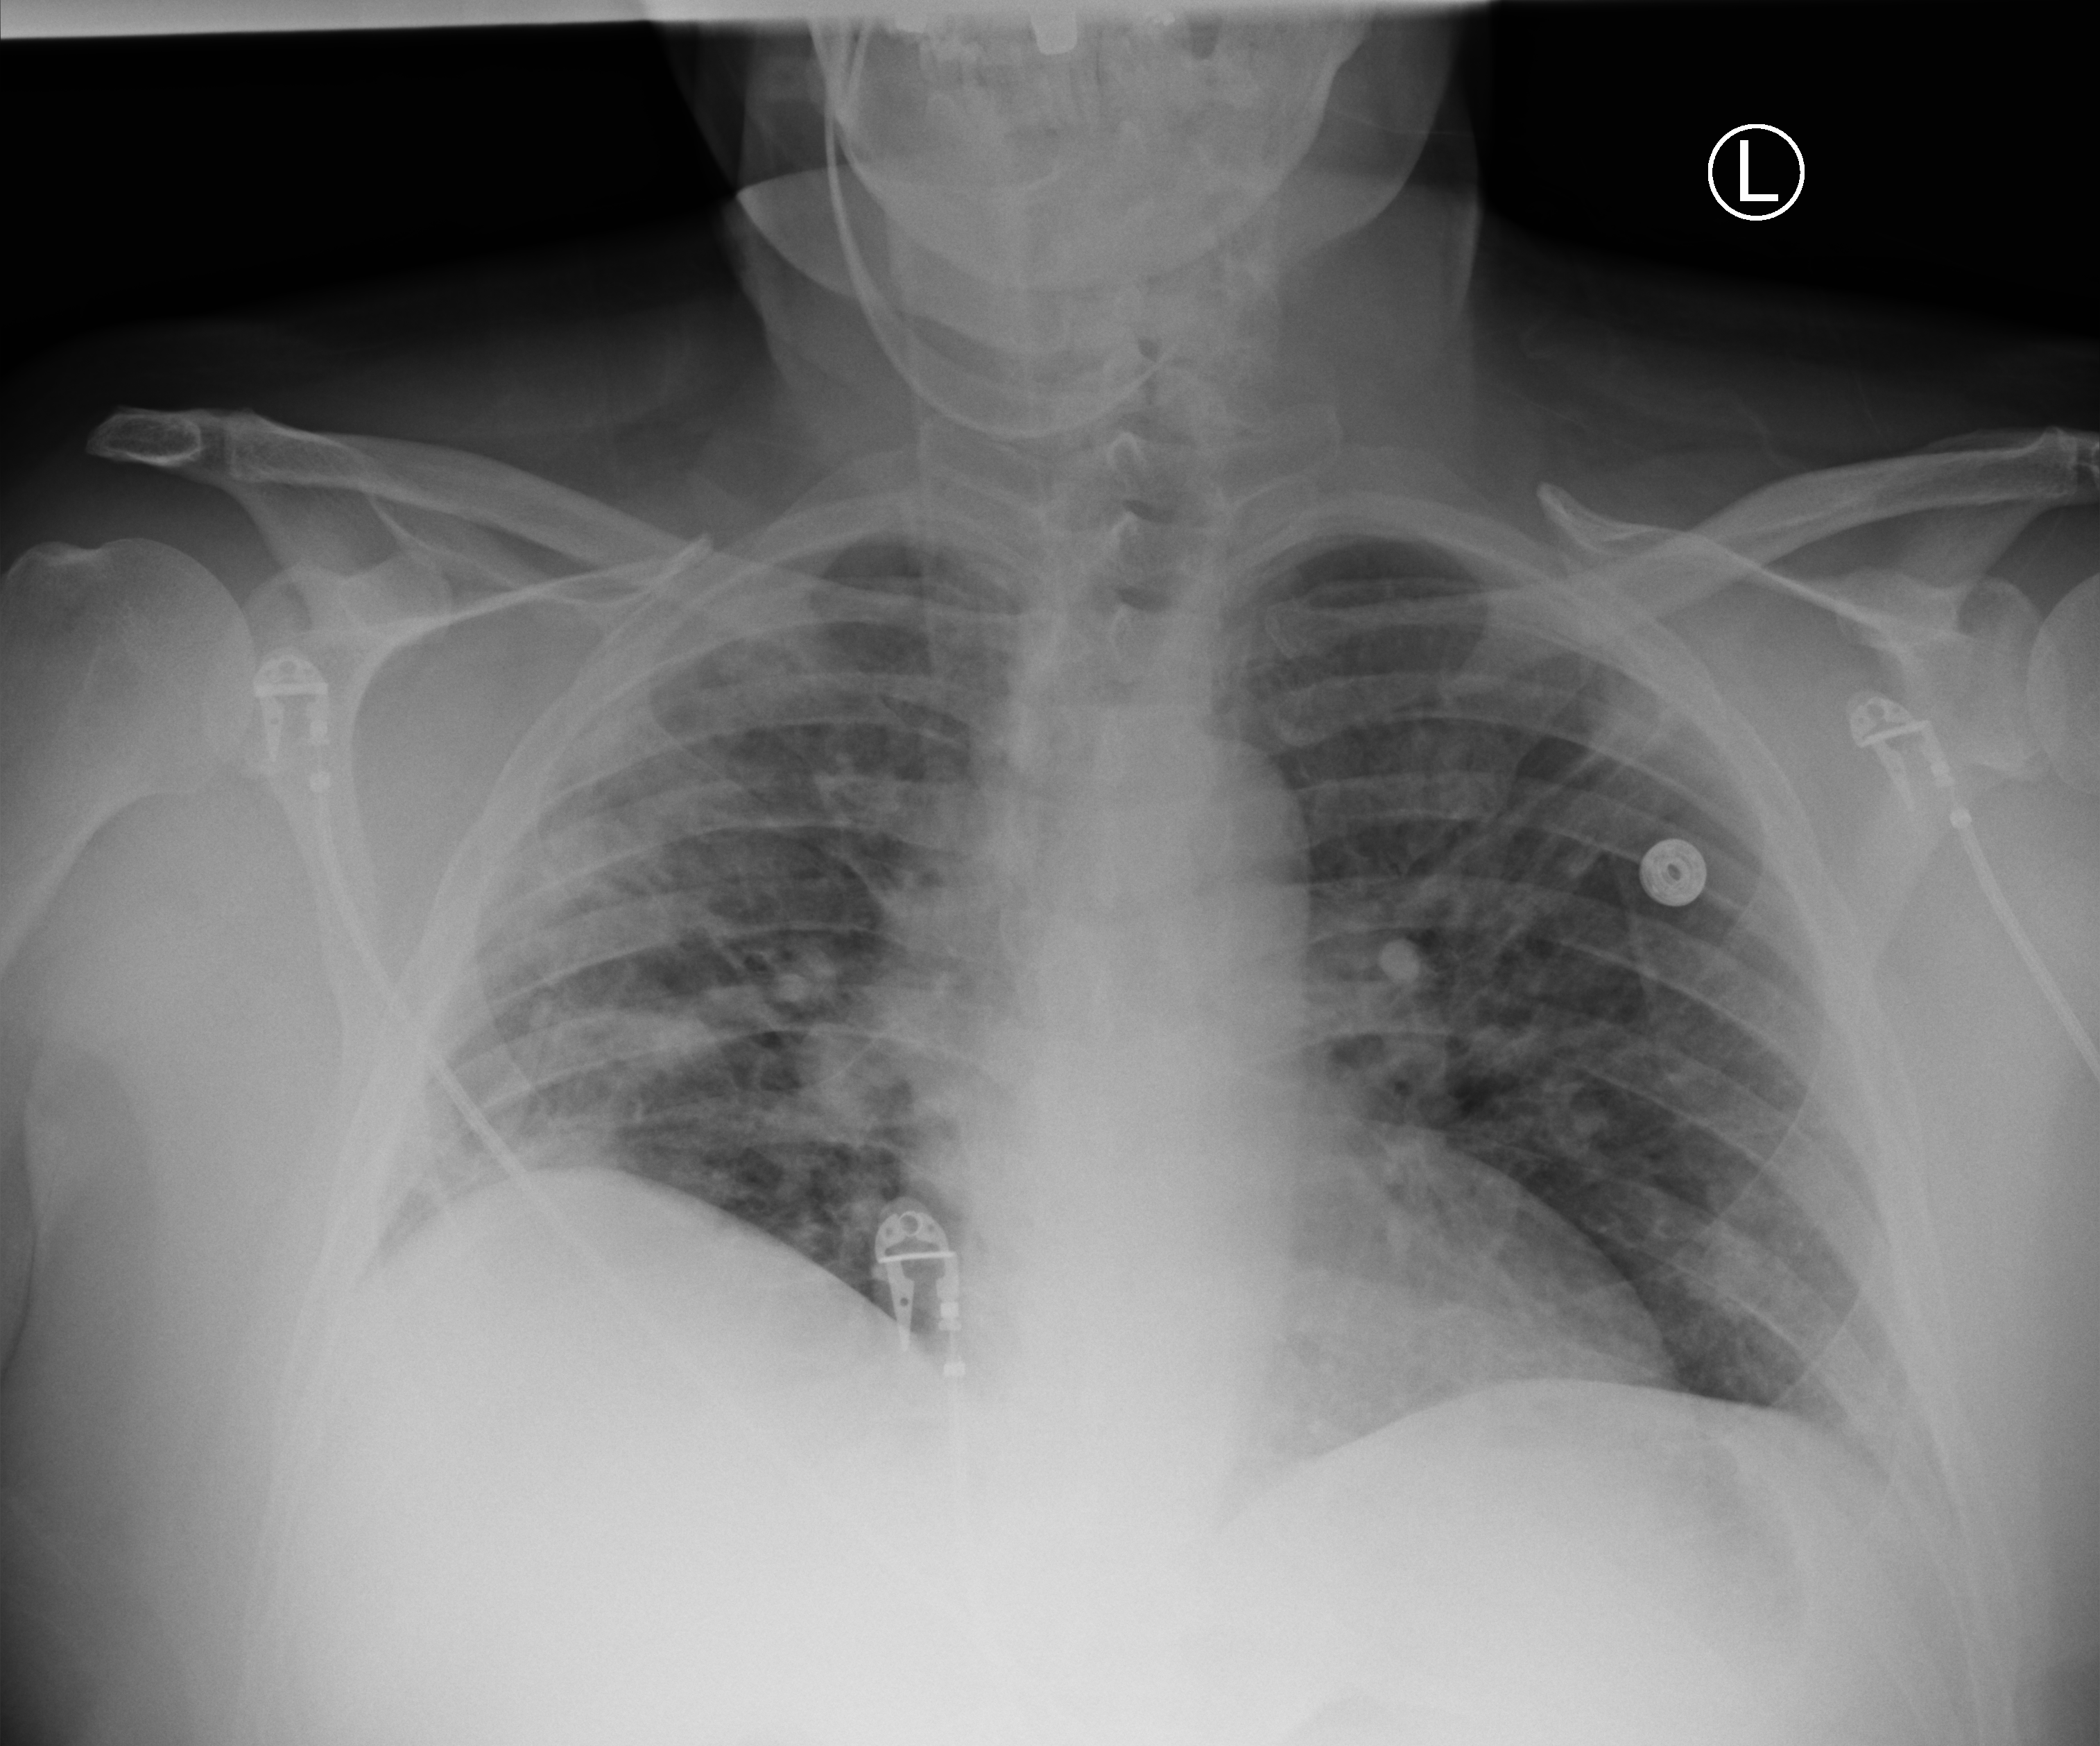
Portable chest radiograph; anteroposterior (AP) projection. Male patient hospitalised with COVID-19, age 18–59 years.
From the hospital-stay record, not from the radiograph (when in the stay this image was taken is not recorded): COPD (admission record): no.